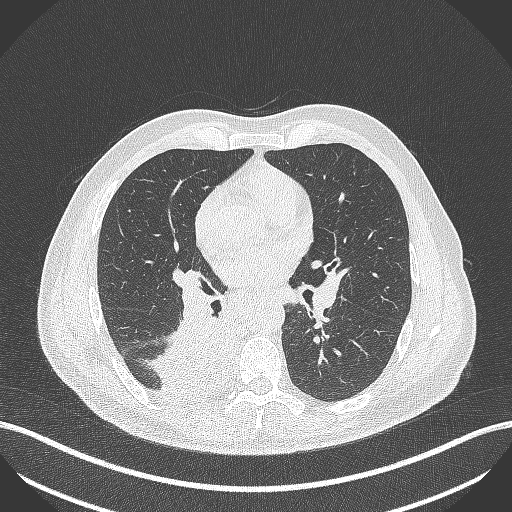
Chest CT, one axial slice. Reconstruction kernel B70f. Lung window (W 1500 / L -600 HU). 1 mm slice thickness. 512 × 512 image matrix. Male patient, age 61 years. From the clinical record (not read from this slice): clinical TNM (as recorded): T1 N0 M0; histopathological grade: G3.
Structures marked on this image (bounding box drawn by a radiologist):
- lung tumour (recorded histology: small cell carcinoma): bounding box <155,307,246,405> (left, top, right, bottom; pixels)